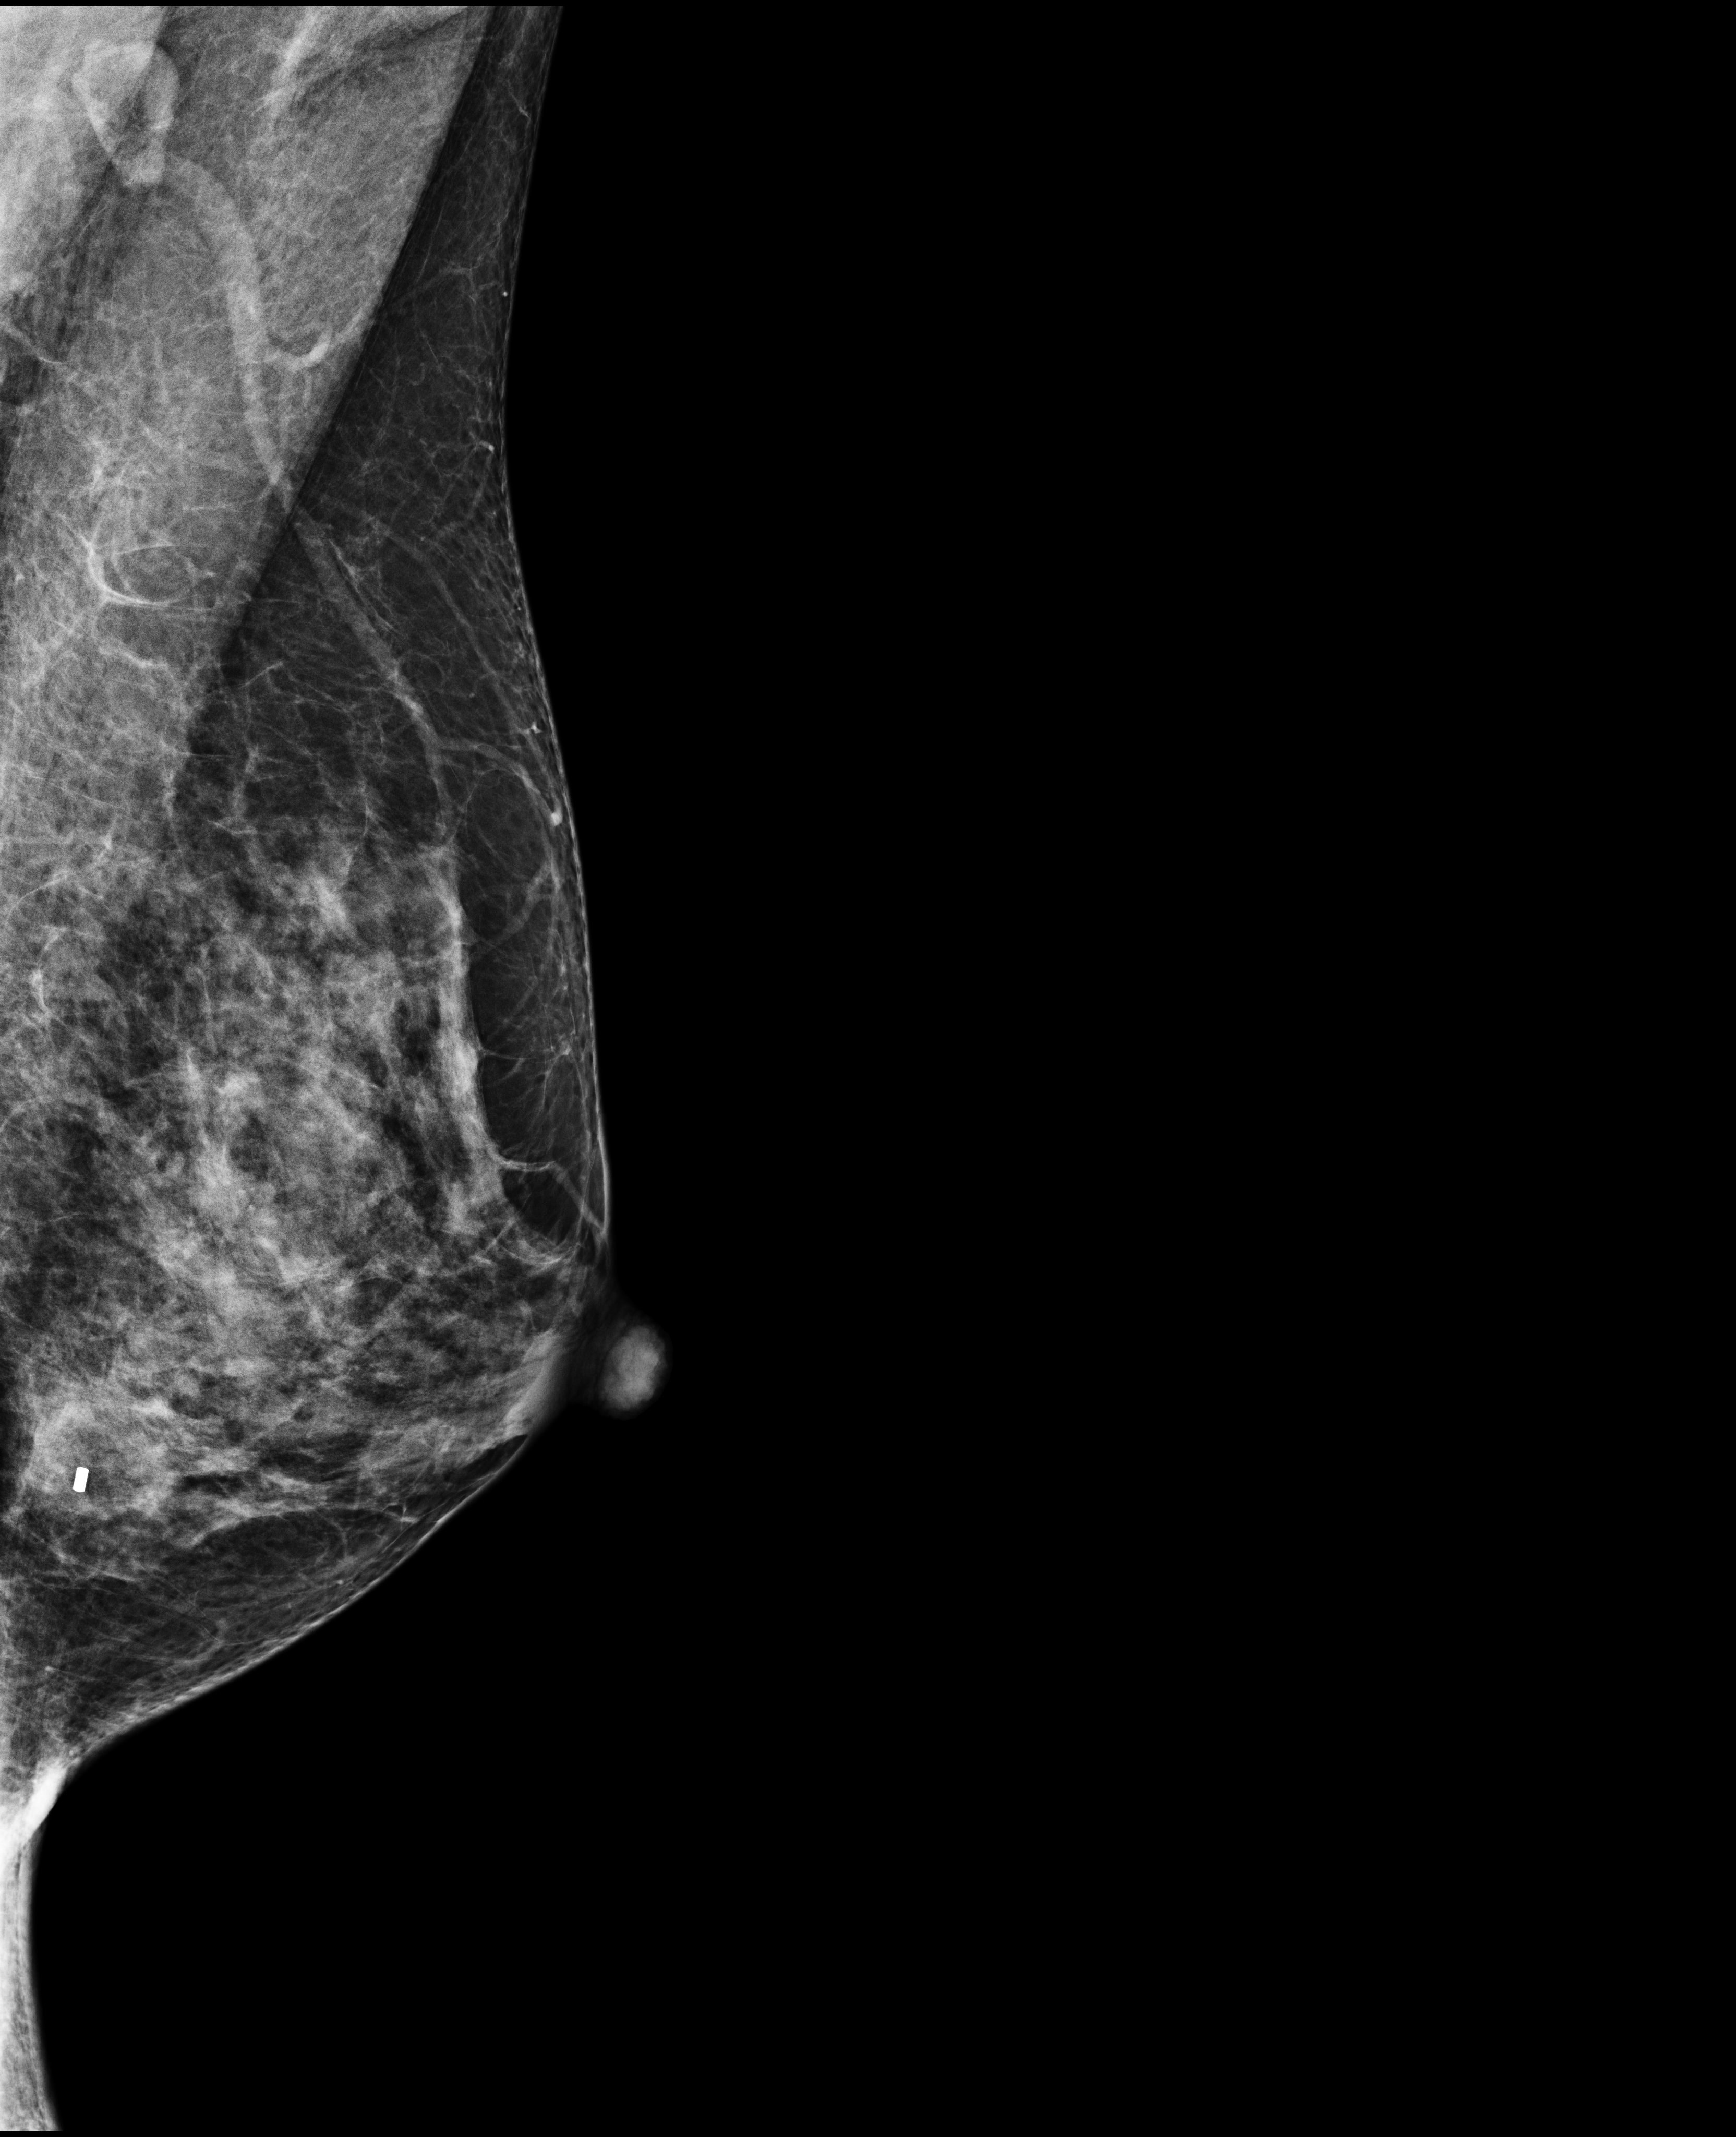
Annual screening mammography examination. Female patient, age 42 years.
Image type: full-field digital mammogram. Breast: left. Projection: medio-lateral oblique projection.